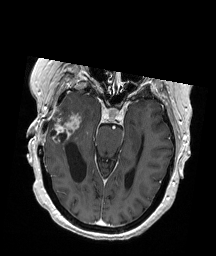
Brain MRI from a brain-tumour surgery series, one axial slice. Position 122 of 192 along the scan axis. T1-weighted post-contrast. 1 mm slice thickness. 216 × 256 image matrix, field of view 211 × 250 mm. From the clinical record (not read from this slice): histopathology: Glioblastoma; WHO grade: 4; IDH mutation: no.
Structures marked on this image (expert manual segmentation):
- tumour: bounding box <49,114,81,132> (left, top, right, bottom; pixels)